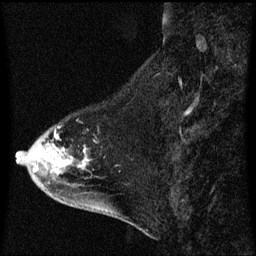
Breast MRI (dynamic contrast-enhanced), one sagittal slice; position 20 of 60 along the scan axis; dynamic contrast-enhanced series, image 2 of 3 at this slice position (ordered by acquisition); 1.5 T; TE 4.2 ms, TR 8.4 ms; 256 × 256 image matrix, field of view 200 × 200 mm. Female patient, age 46 years. Case-level facts recorded for this patient, not image findings: setting: breast cancer imaged before/during neoadjuvant chemotherapy; receptor status: HER2-positive.
Annotated regions visible in this slice (semi-automatically segmented with operator editing):
- analysis volume of interest (the breast-tissue region the enhancement analysis was run in; not a lesion): box from (x=18, y=126) to (x=97, y=195) px
- tumour enhancement mask (voxels above the 70 % enhancement threshold inside the analysis volume of interest): (x=56, y=136)–(x=85, y=165)